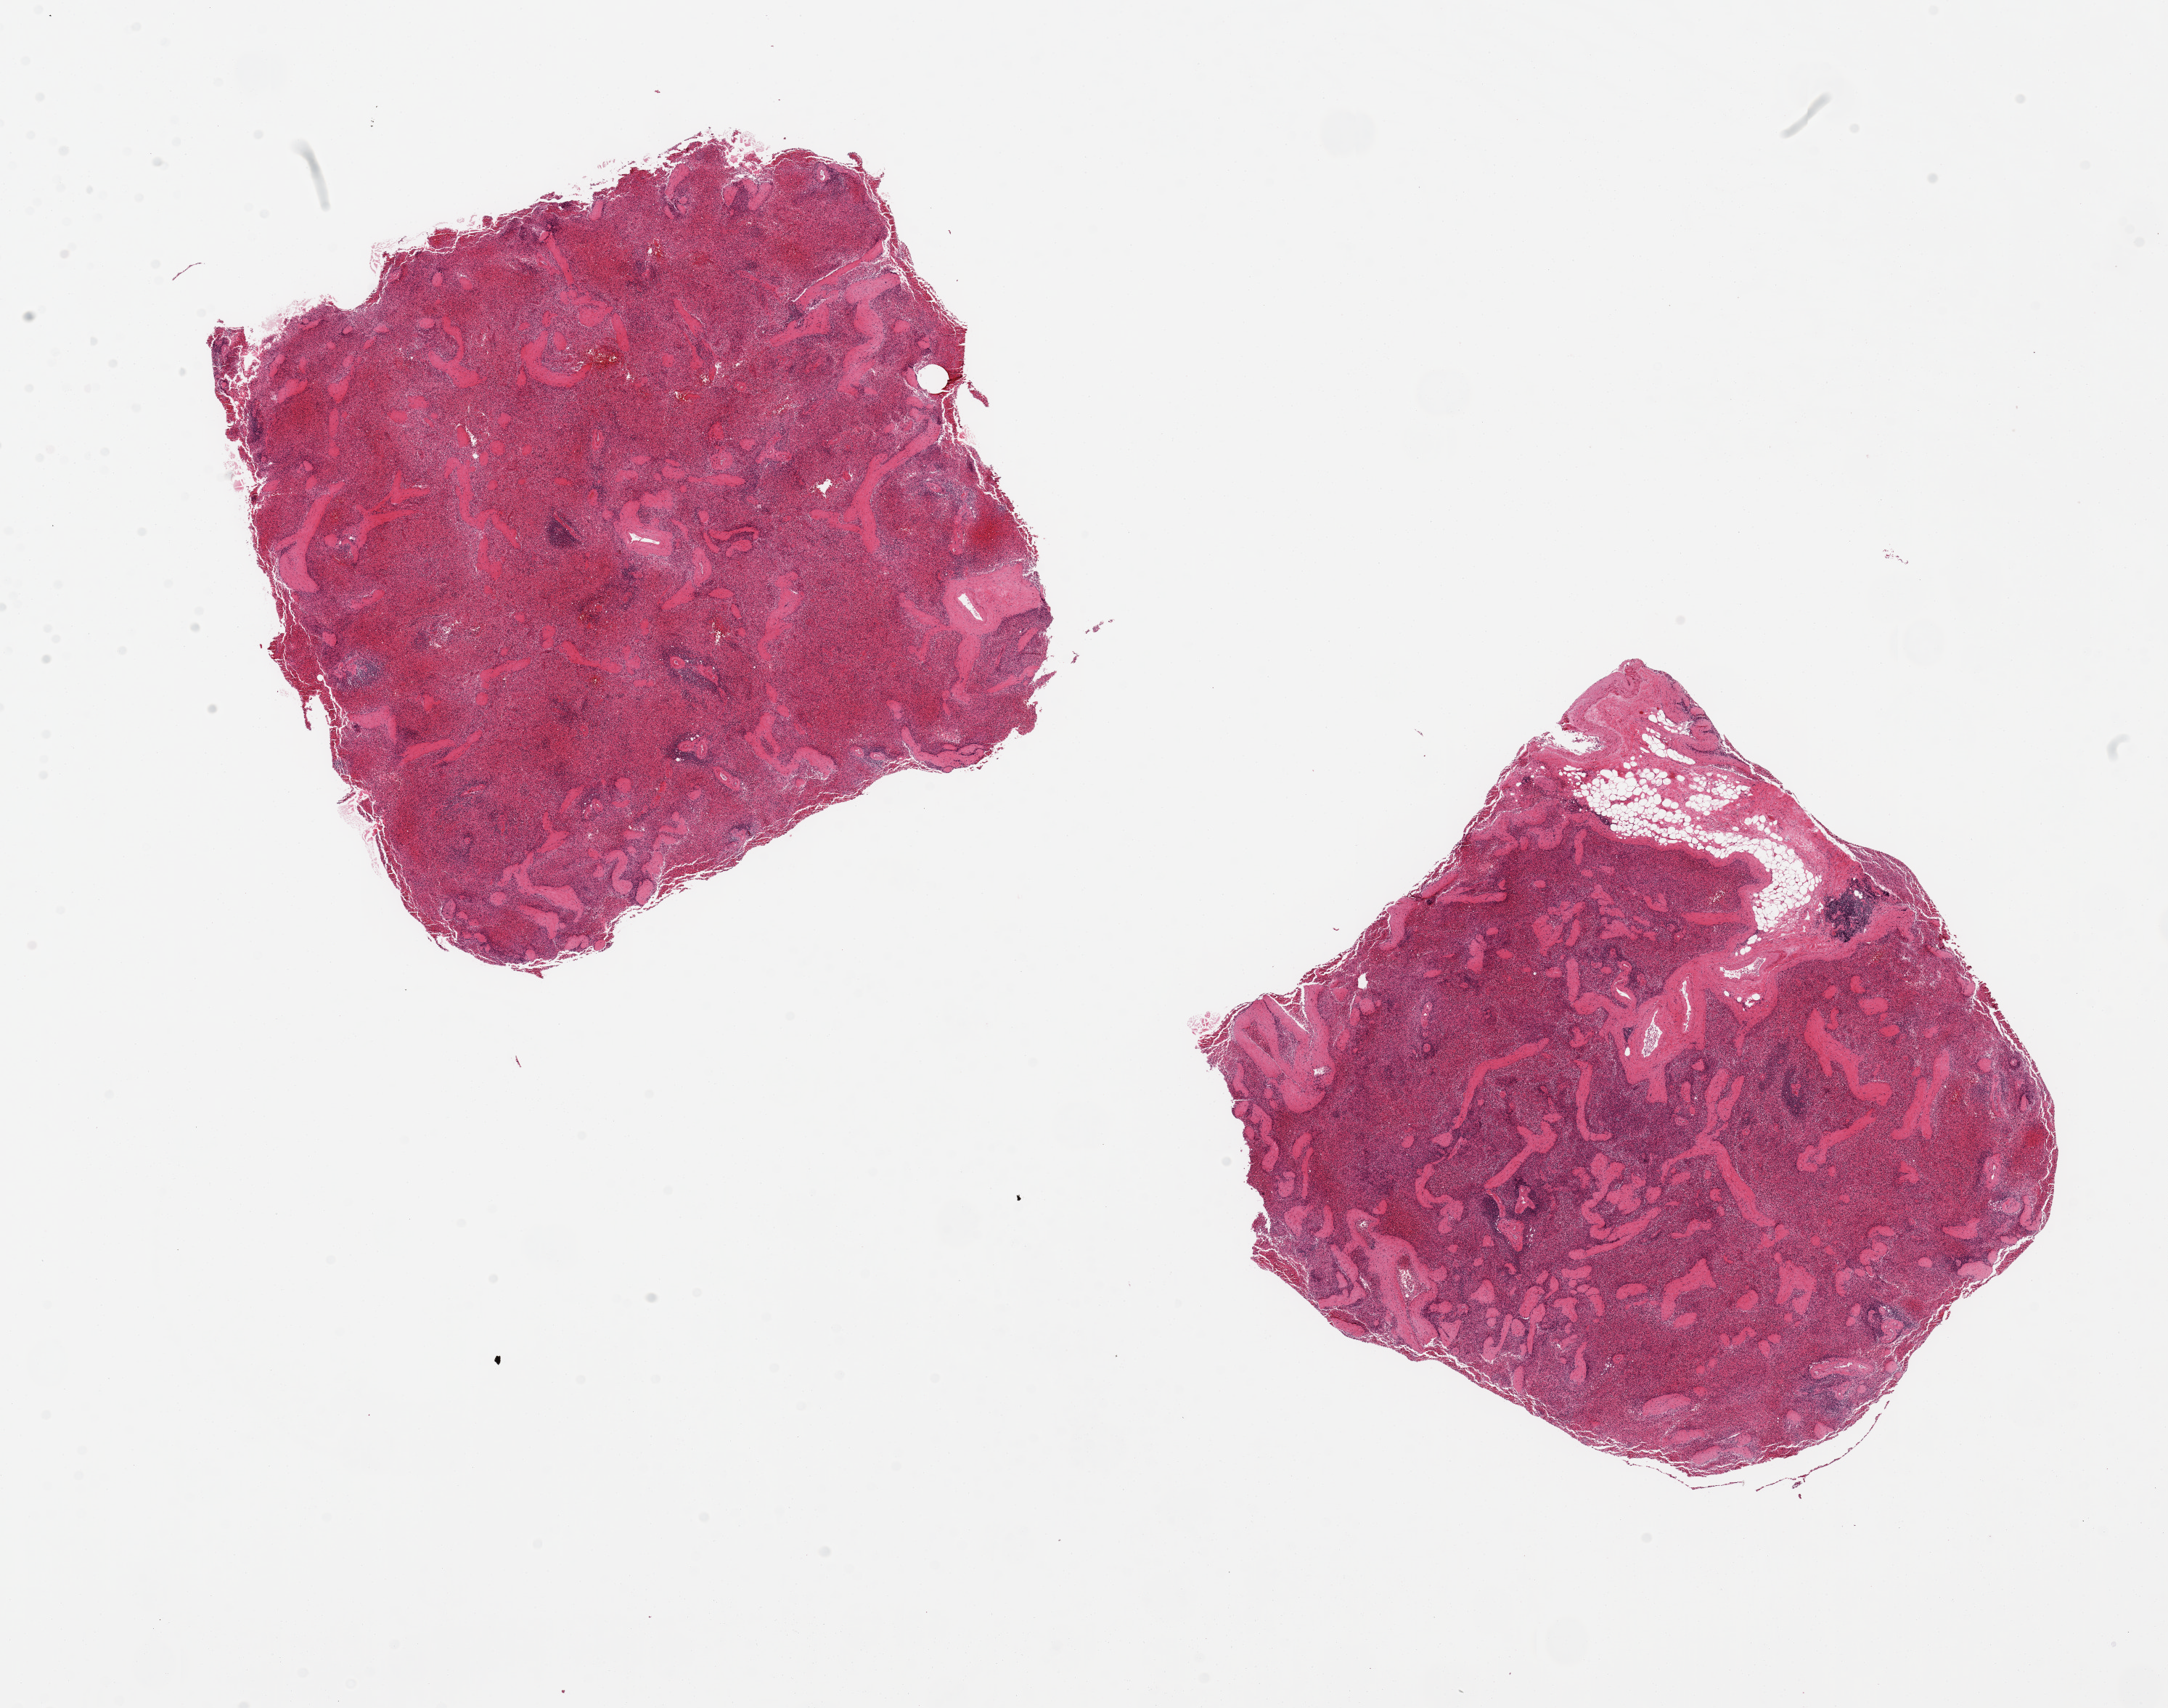
Digitized hematoxylin and eosin (H&E)-stained section, low-resolution overview of the scanned area, about 23.6 x 18.6 mm; PAXgene-fixed paraffin-embedded (PFPE) section; target tissue: spleen; tissue donor sample. Donor: female.
Review note (as recorded): 2 pieces. 8x8 & 8.5x8mm; congested.